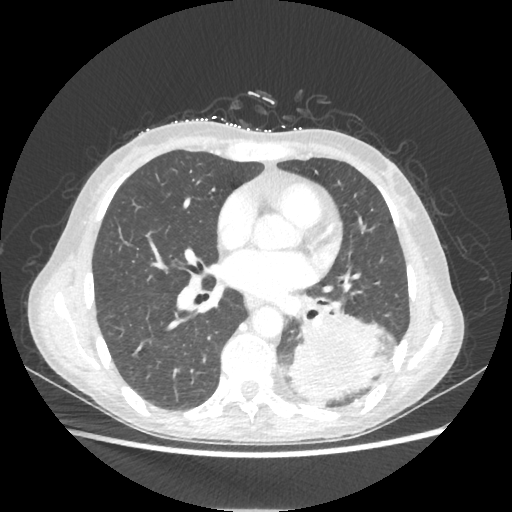
Chest CT, one axial slice; slice 104 of 221 in the series (ordered by position); reconstruction kernel STANDARD; 80 kVp; lung window (W 1500 / L -600 HU); 1.25 mm slice thickness; 512 × 512 image matrix, field of view 360 × 360 mm. Patient: female, 53 years. Case-level facts recorded for this patient, not image findings: clinical TNM (as recorded): T3 N0 M0.
Annotated regions visible in this slice (rectangle marked by the reading radiologist):
- lung tumour (recorded histology: adenocarcinoma): bounding box <285,313,386,403> (left, top, right, bottom; pixels)